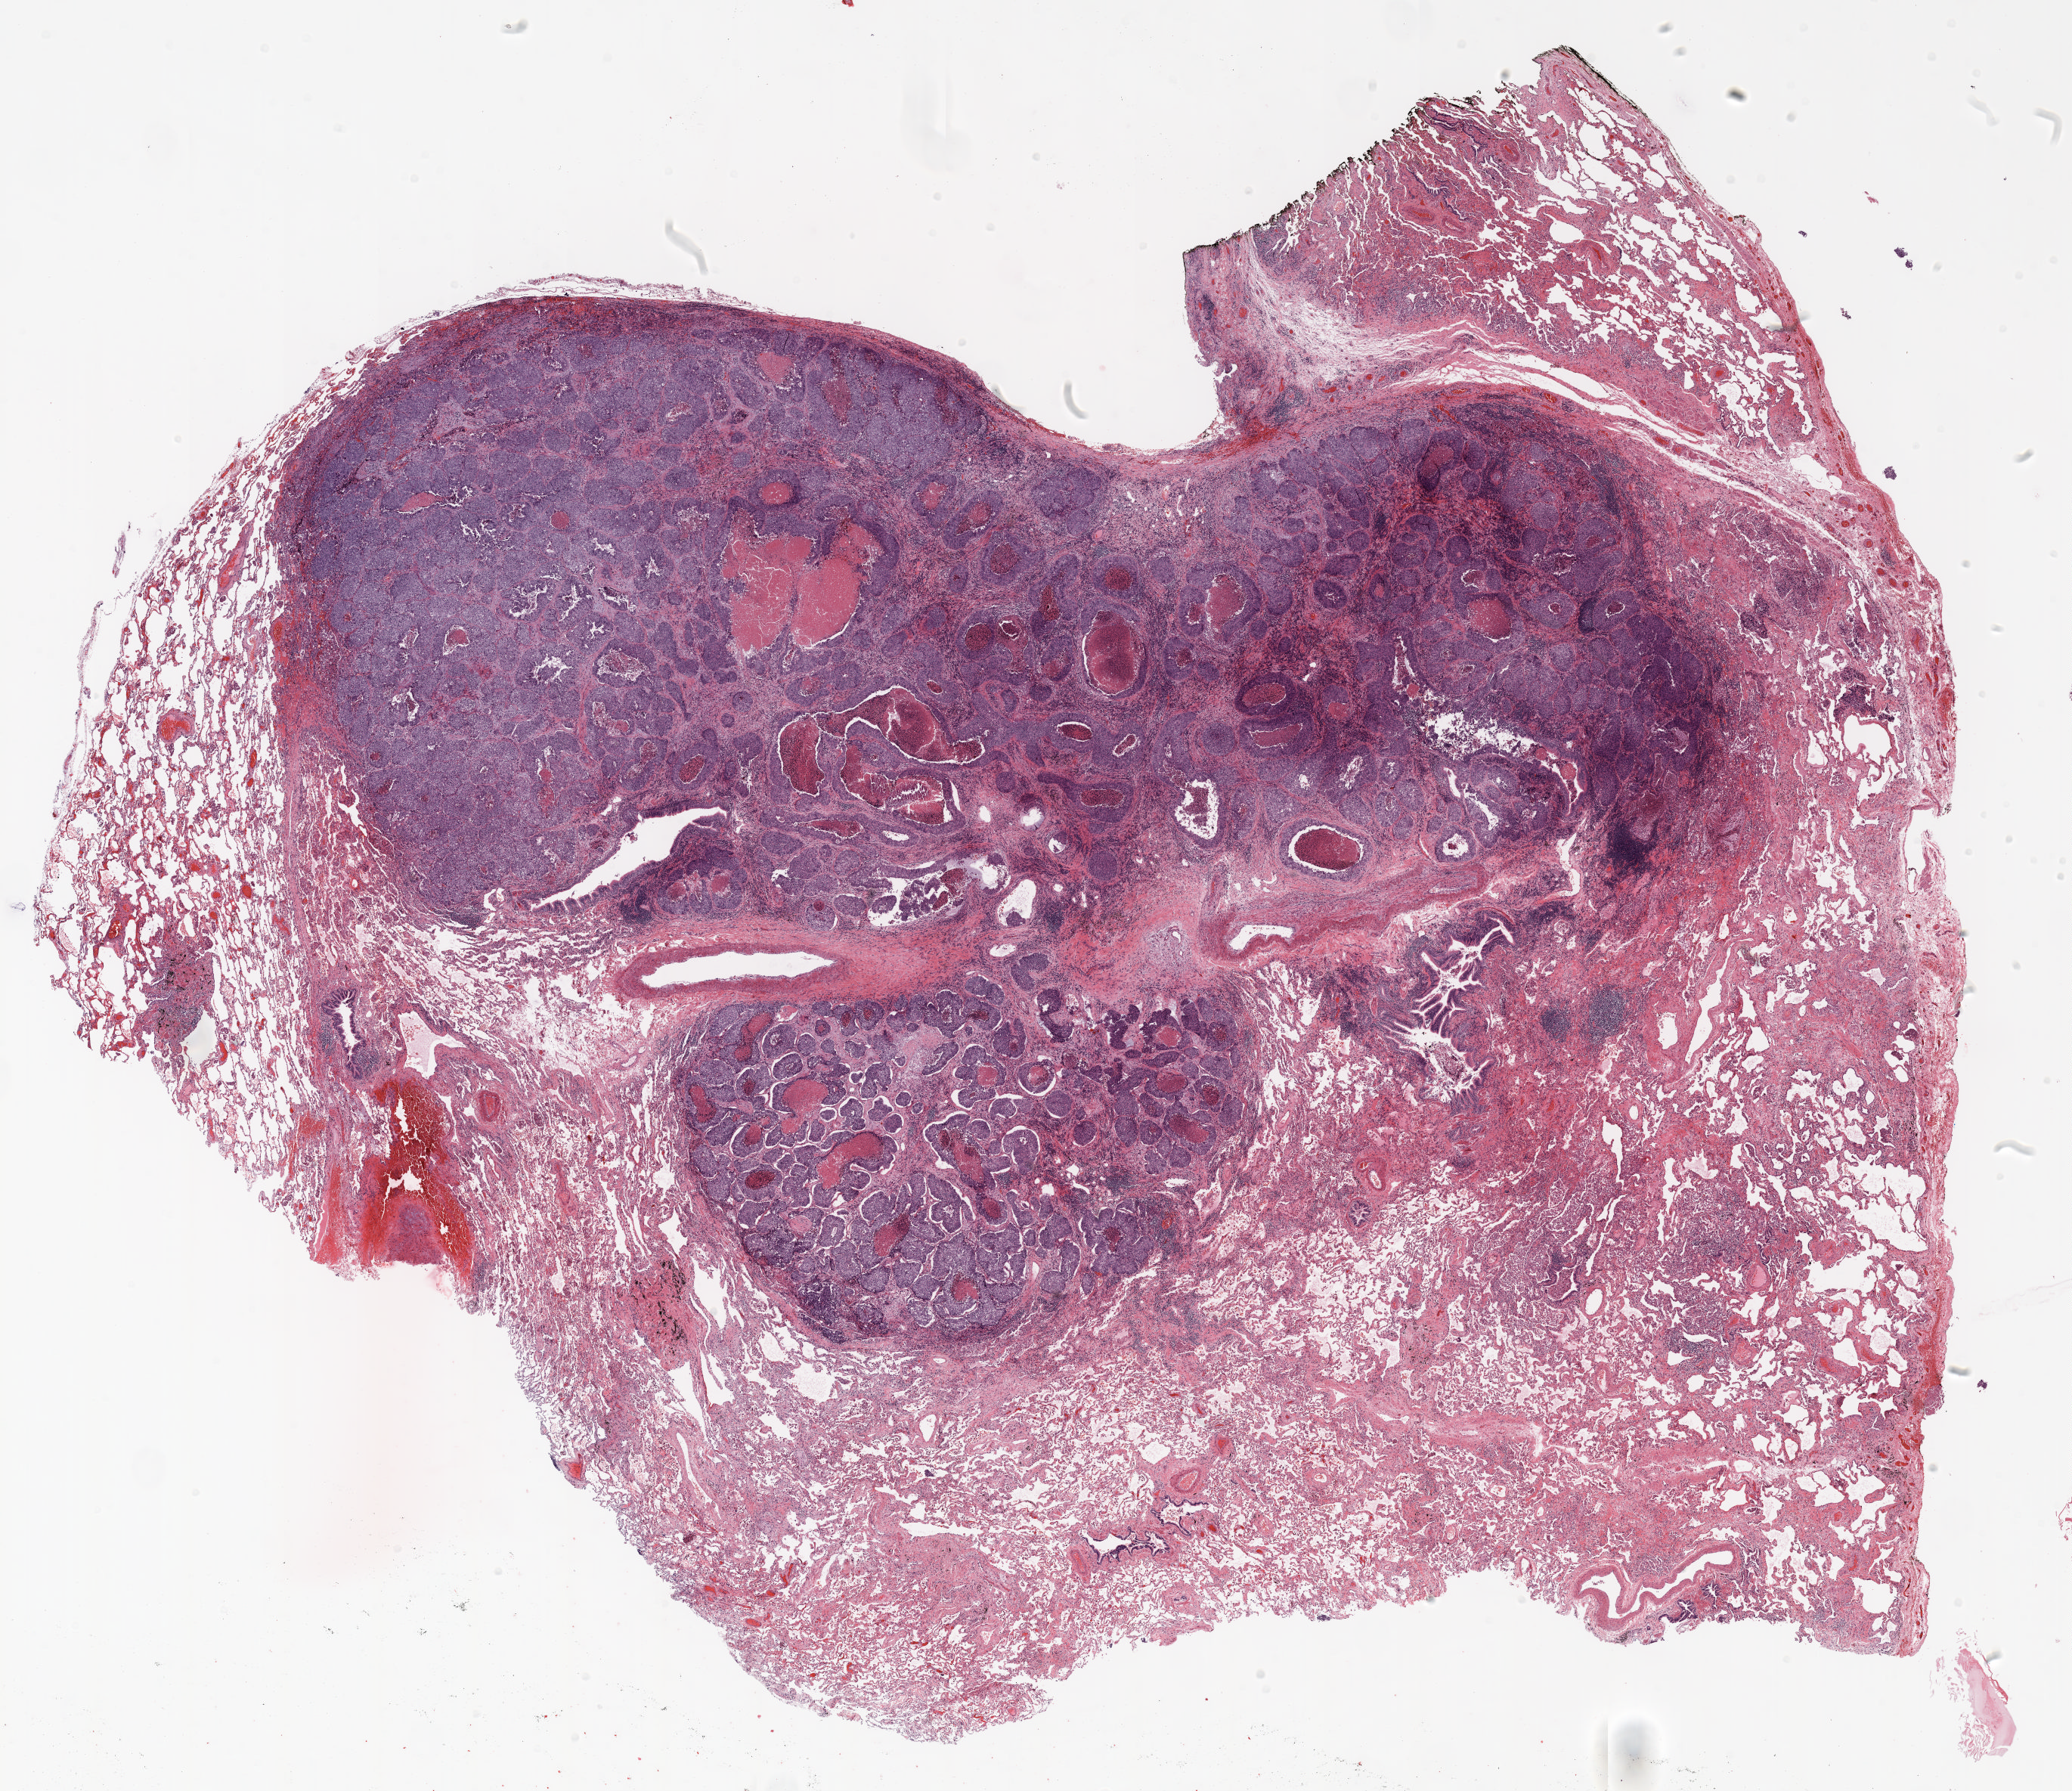
Whole-slide histology image, H&E-stained, low-resolution overview of the scanned area, about 22.0 x 19.0 mm, formalin-fixed paraffin-embedded (FFPE) section, lung tissue. Male patient, aged 61 at enrolment. Former smoker at enrolment.
Participant's lung-cancer diagnosis: Adenocarcinoma, NOS (ICD-O-3 8140/3).